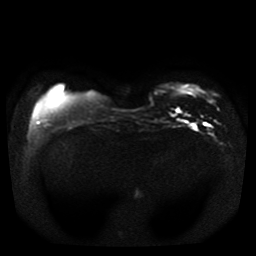
Breast MRI, one axial slice; slice 7 of 41 in the series (ordered by position); diffusion-weighted series; image 2 of 4 stored at this slice position (different b-values; order by instance number); 1.5 T; 256 × 256 image matrix. Female patient.
Structures marked on this image (outlined manually by an expert reader):
- tumour on diffusion-weighted imaging: box from (x=210, y=100) to (x=213, y=103) px